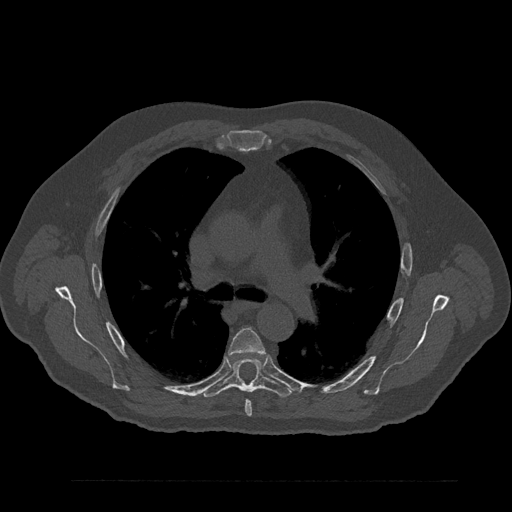
CT including the spine, one axial slice. Reconstruction kernel Br40s/3. Bone window (W 1800 / L 400 HU). 0.5 mm slice thickness. 512 × 512 image matrix, field of view 430 × 430 mm. Male patient, age 61 years. Case-level facts recorded for this patient, not image findings: primary cancer: prostate.
Outlined on this slice (semi-automatic segmentation, software-assisted and operator-edited):
- T5 vertebra: bounding box (x1, y1, x2, y2) in pixels: (228, 328, 265, 416)
- T6 vertebra: (201, 357, 293, 398)